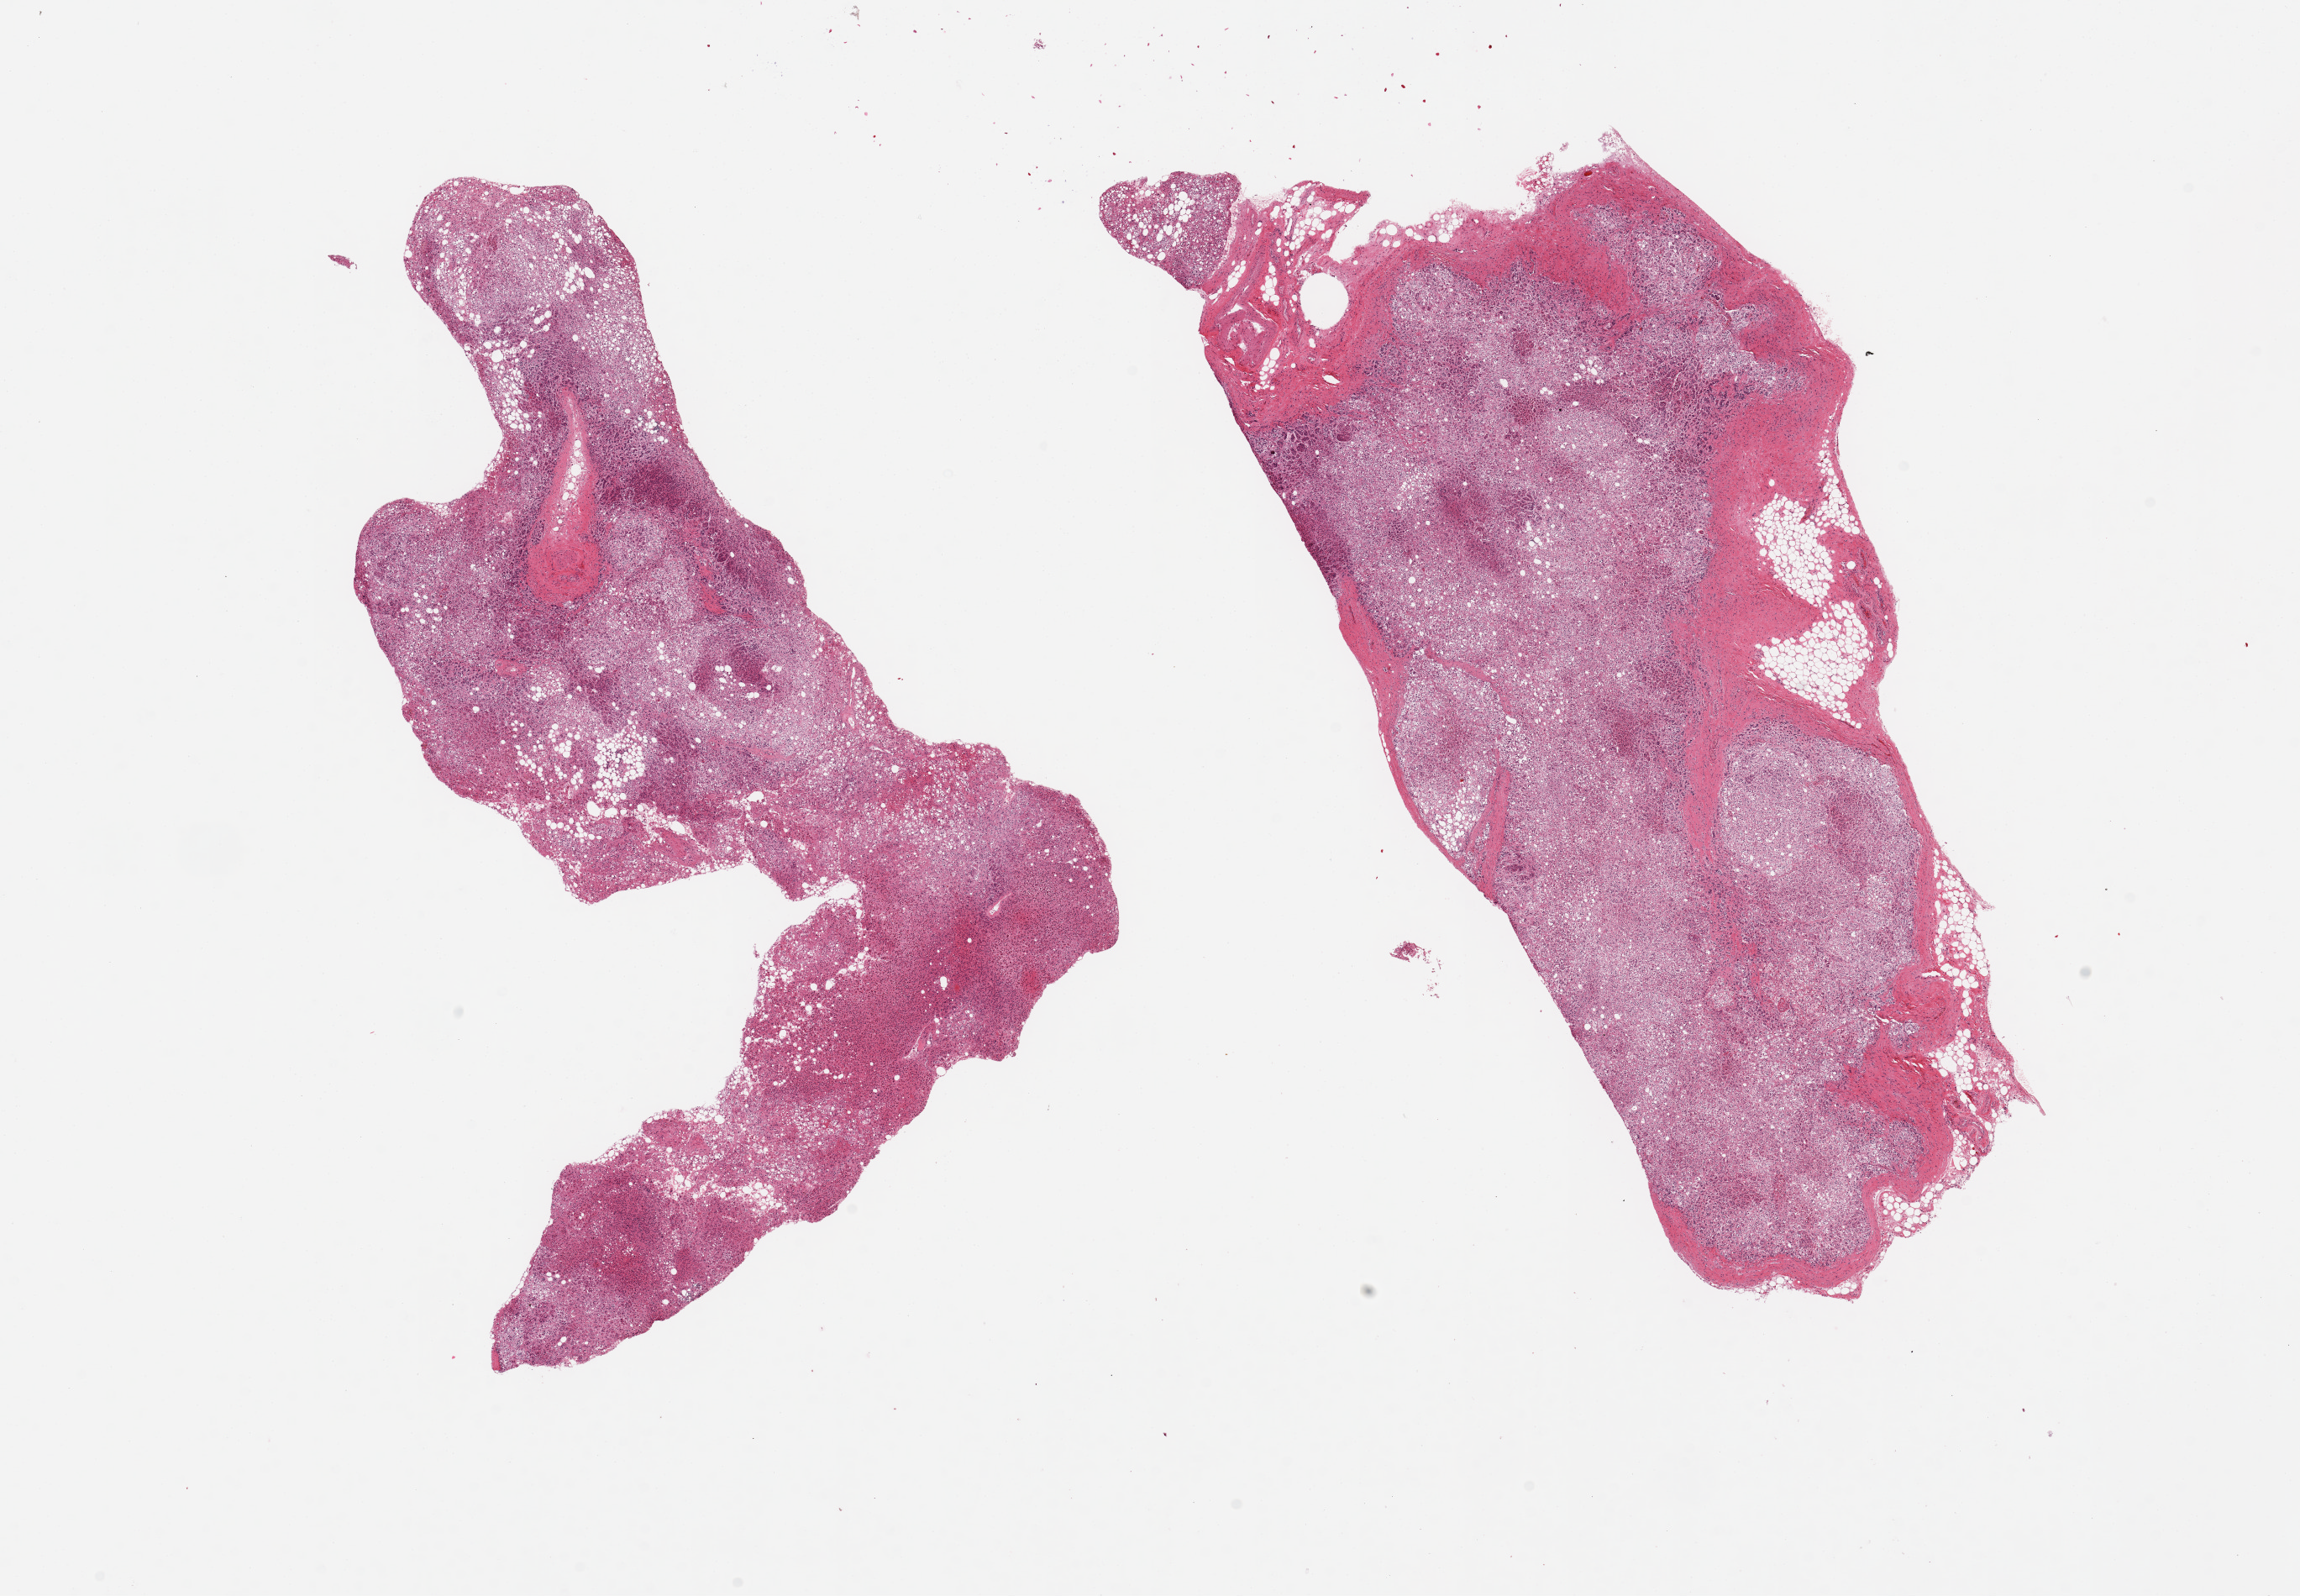
Haematoxylin and eosin whole-slide image, whole scanned area (about 21.7 x 15.0 mm) shown as a low-resolution overview. PAXgene-fixed paraffin-embedded (PFPE) section. Section of adrenal gland (target tissue). Donor tissue sample.
Pathologist's review note for this sample: 2 pieces; small amount of external fat.